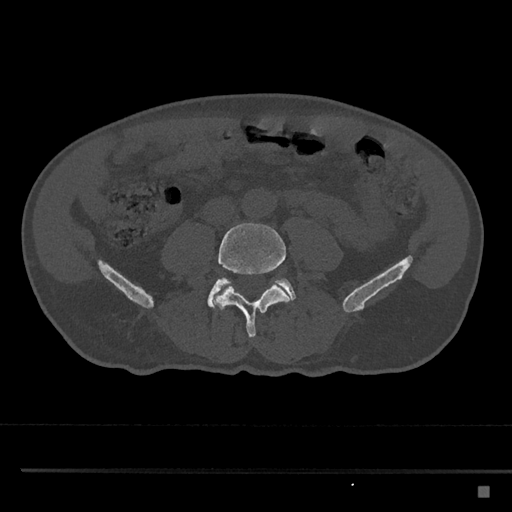
CT including the spine, one axial slice; position 622 of 797 along the scan axis; reconstruction kernel Br40s/3; 120 kVp; bone window (W 1800 / L 400 HU); 512 × 512 image matrix, field of view 391 × 391 mm. Male patient, age 59 years. From the clinical record (not read from this slice): primary cancer: prostate.
Structures marked on this image (semi-automatically segmented with operator editing):
- L4 vertebra: bounding box <214,223,290,338> (left, top, right, bottom; pixels)
- L5 vertebra: <208,278,296,309>